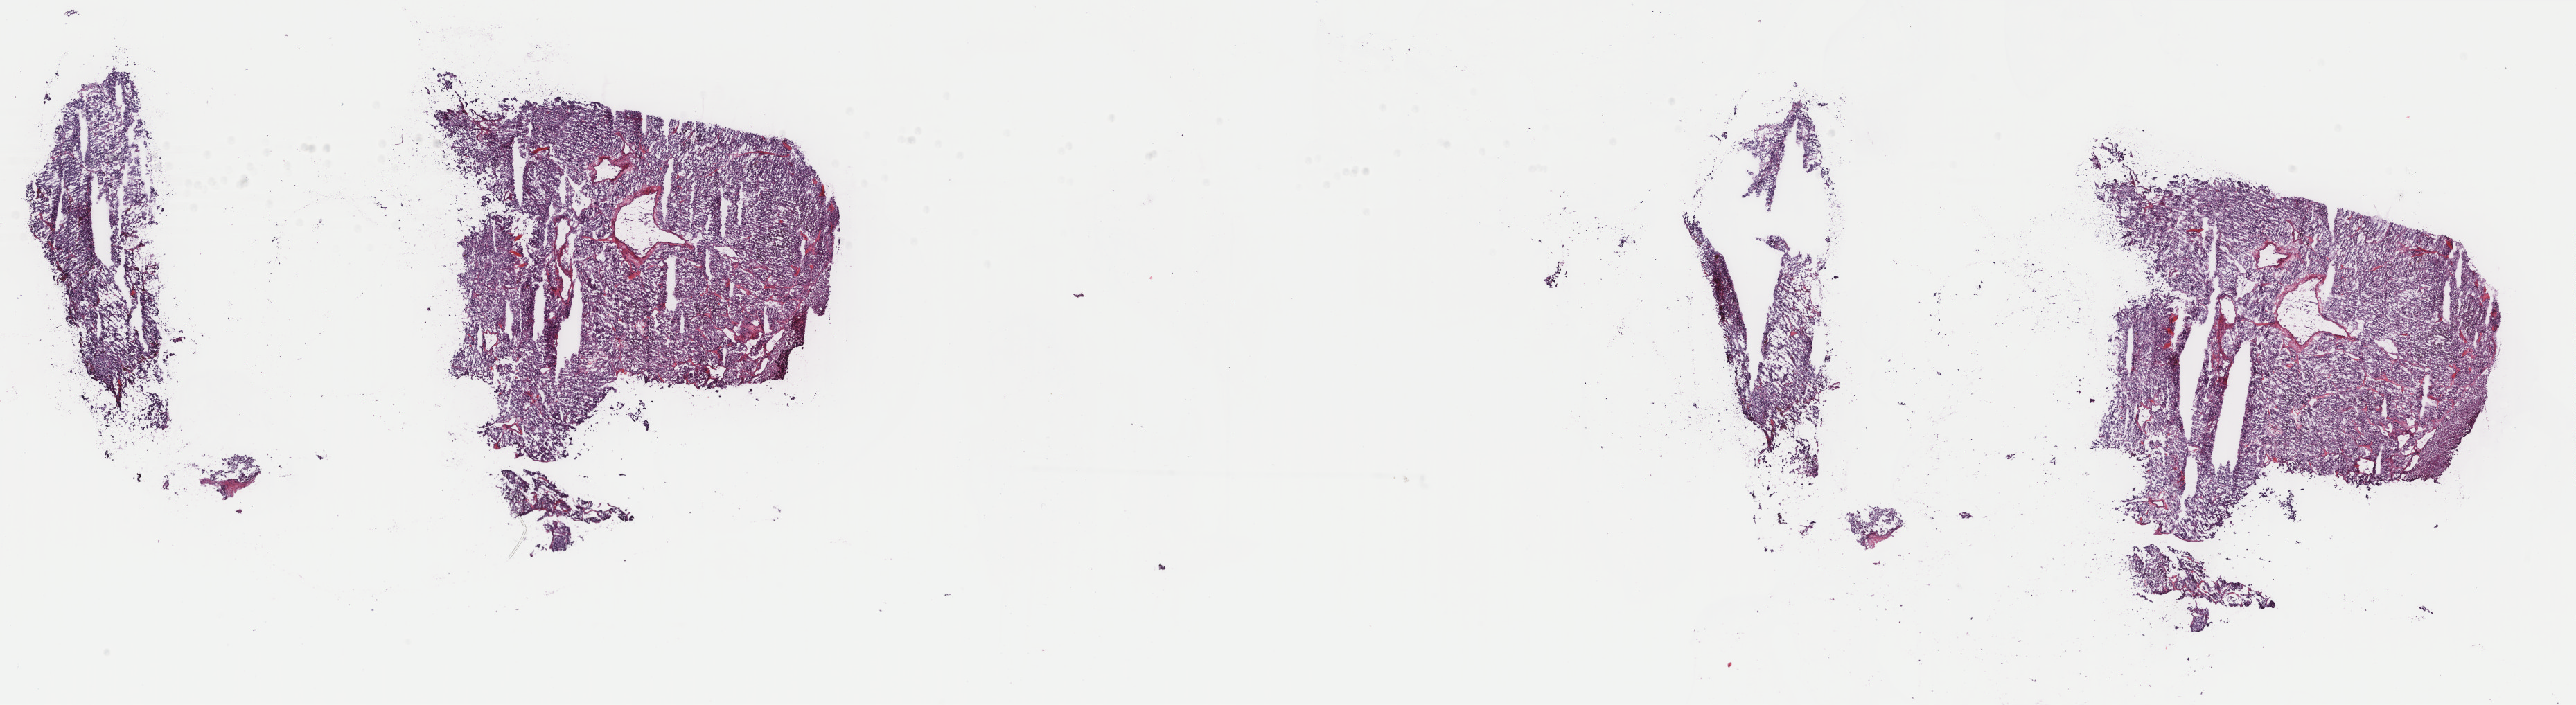
Whole-slide histology image, H&E — low-resolution overview of the scanned area, about 29.5 x 8.1 mm (from a 40x scan). Frozen section from the top of the tissue portion. Sample: primary tumour, adrenal gland. Patient: female, age at initial diagnosis 50 years. Composition of this section per pathologist review: tumour cells 80%, tumour nuclei 80%, normal cells 0%, stromal cells 10%, necrosis 10%. Infiltration values recorded for this section: lymphocyte infiltration 40%, monocyte infiltration 20%, neutrophil infiltration 20%.
Diagnosis: Pheochromocytoma, NOS. Laterality: right.